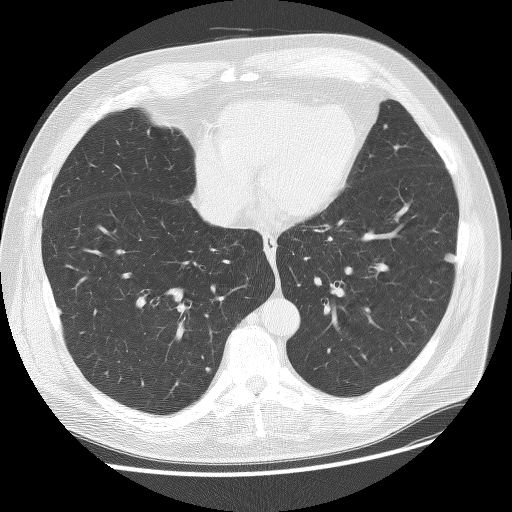
Low-dose screening chest CT, one axial slice; reconstruction kernel BONE; 120 kVp; lung window (W 1500 / L -600 HU); 2.5 mm slice thickness; 512 × 512 image matrix, field of view 380 × 380 mm.
Structures marked on this image (expert manual segmentation):
- lesion 4 (tumor): bounding box <445,254,457,263> (left, top, right, bottom; pixels)